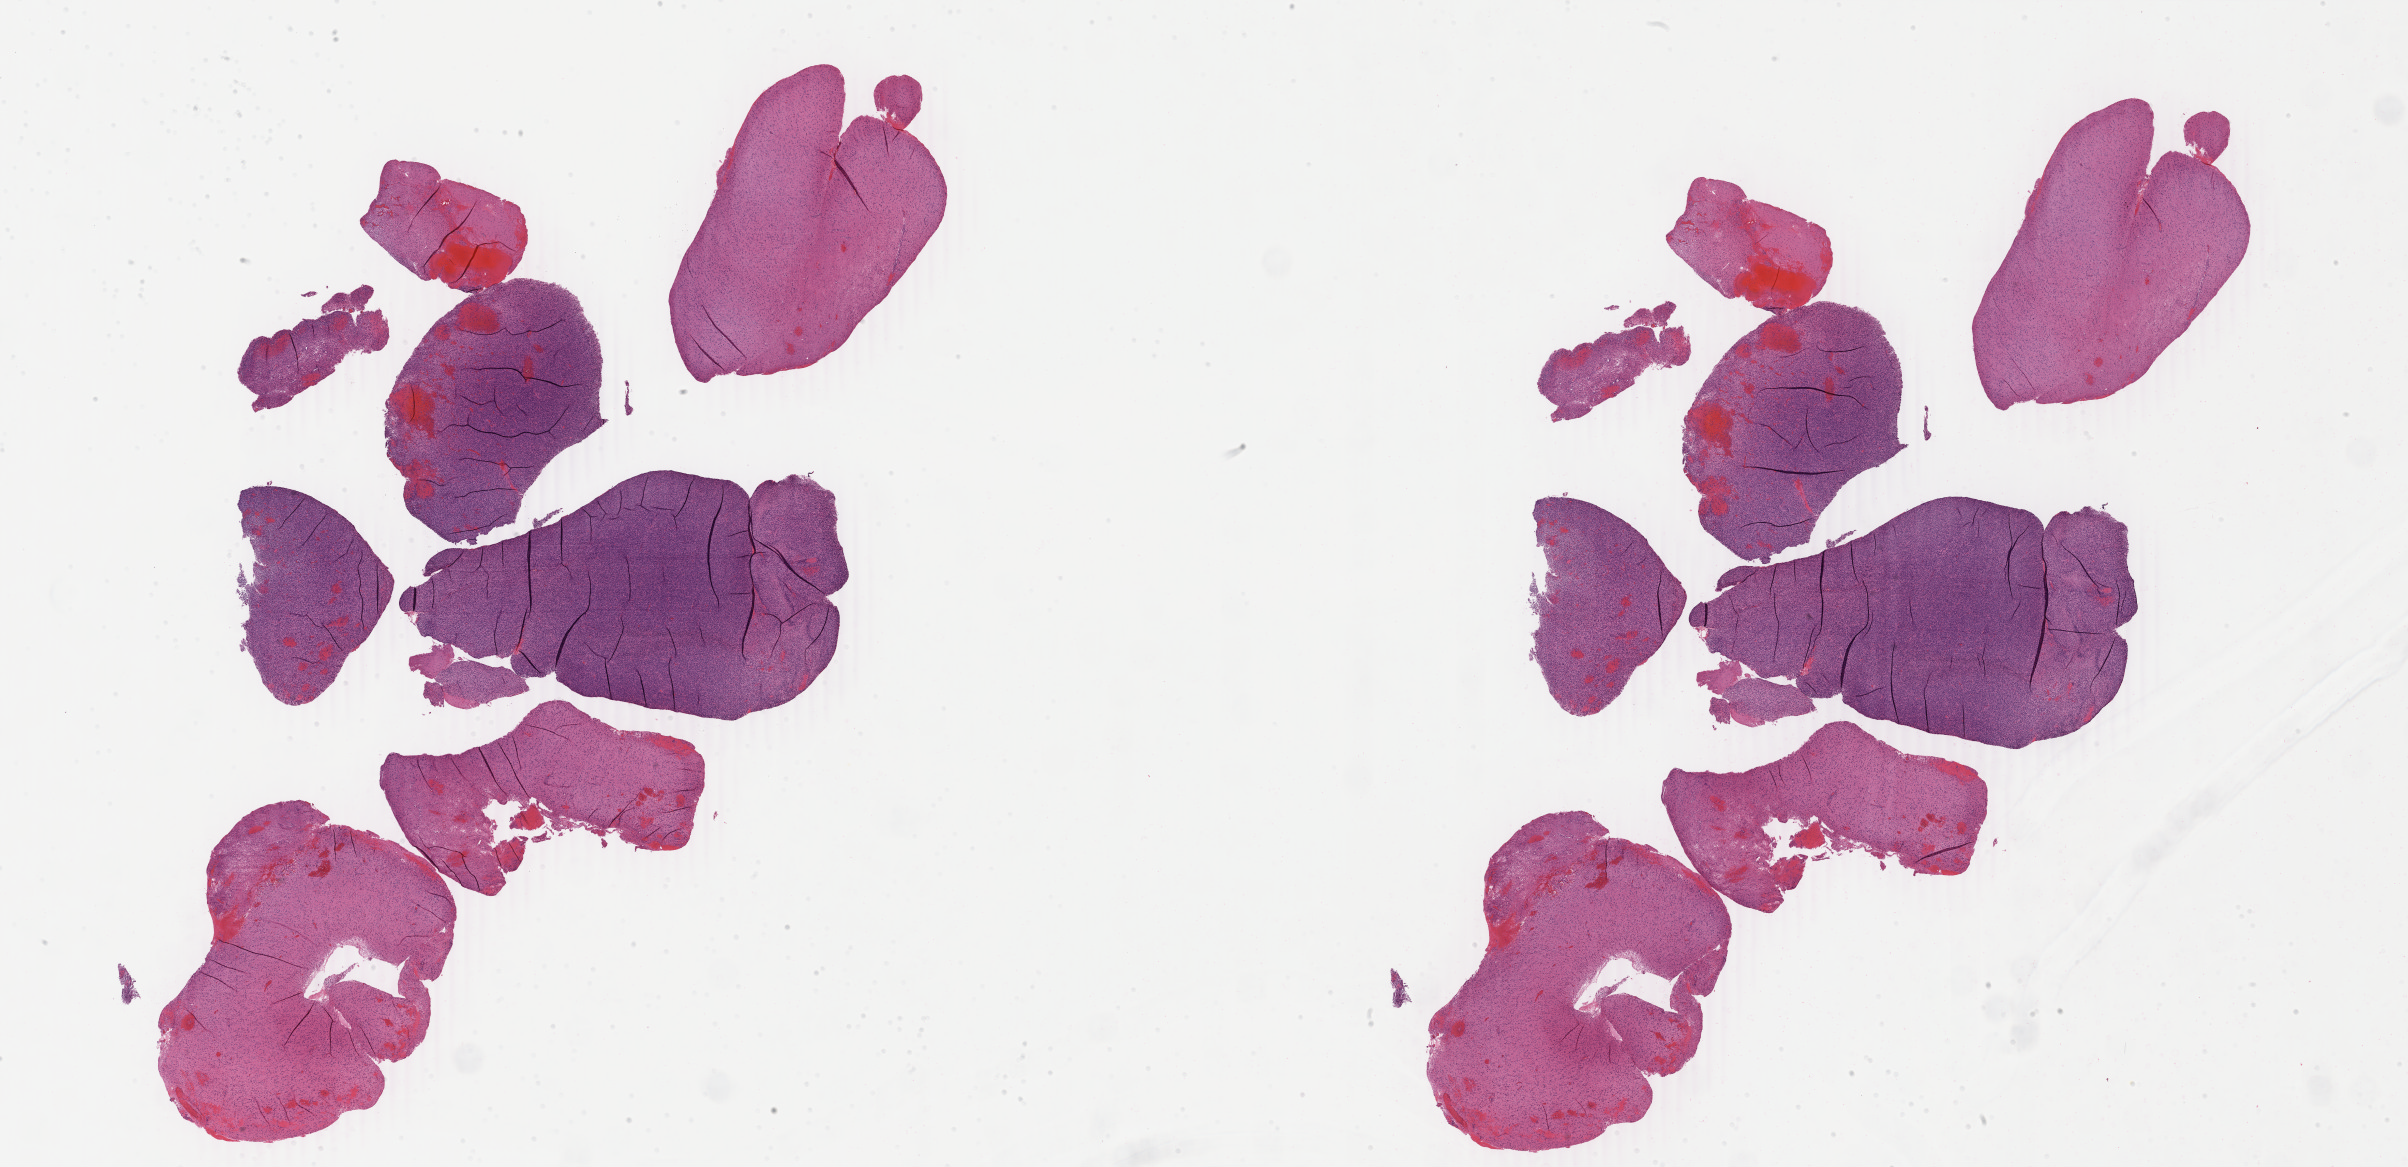
Hematoxylin and eosin (H&E) stained whole-slide image — shown as a low-resolution overview of the whole scanned area (about 38.3 x 18.6 mm, slide scanned at 40x), formalin-fixed paraffin-embedded (FFPE) diagnostic section, sample: primary tumour, brain. Male patient; age at initial diagnosis 47 years.
Diagnosis: Glioblastoma.